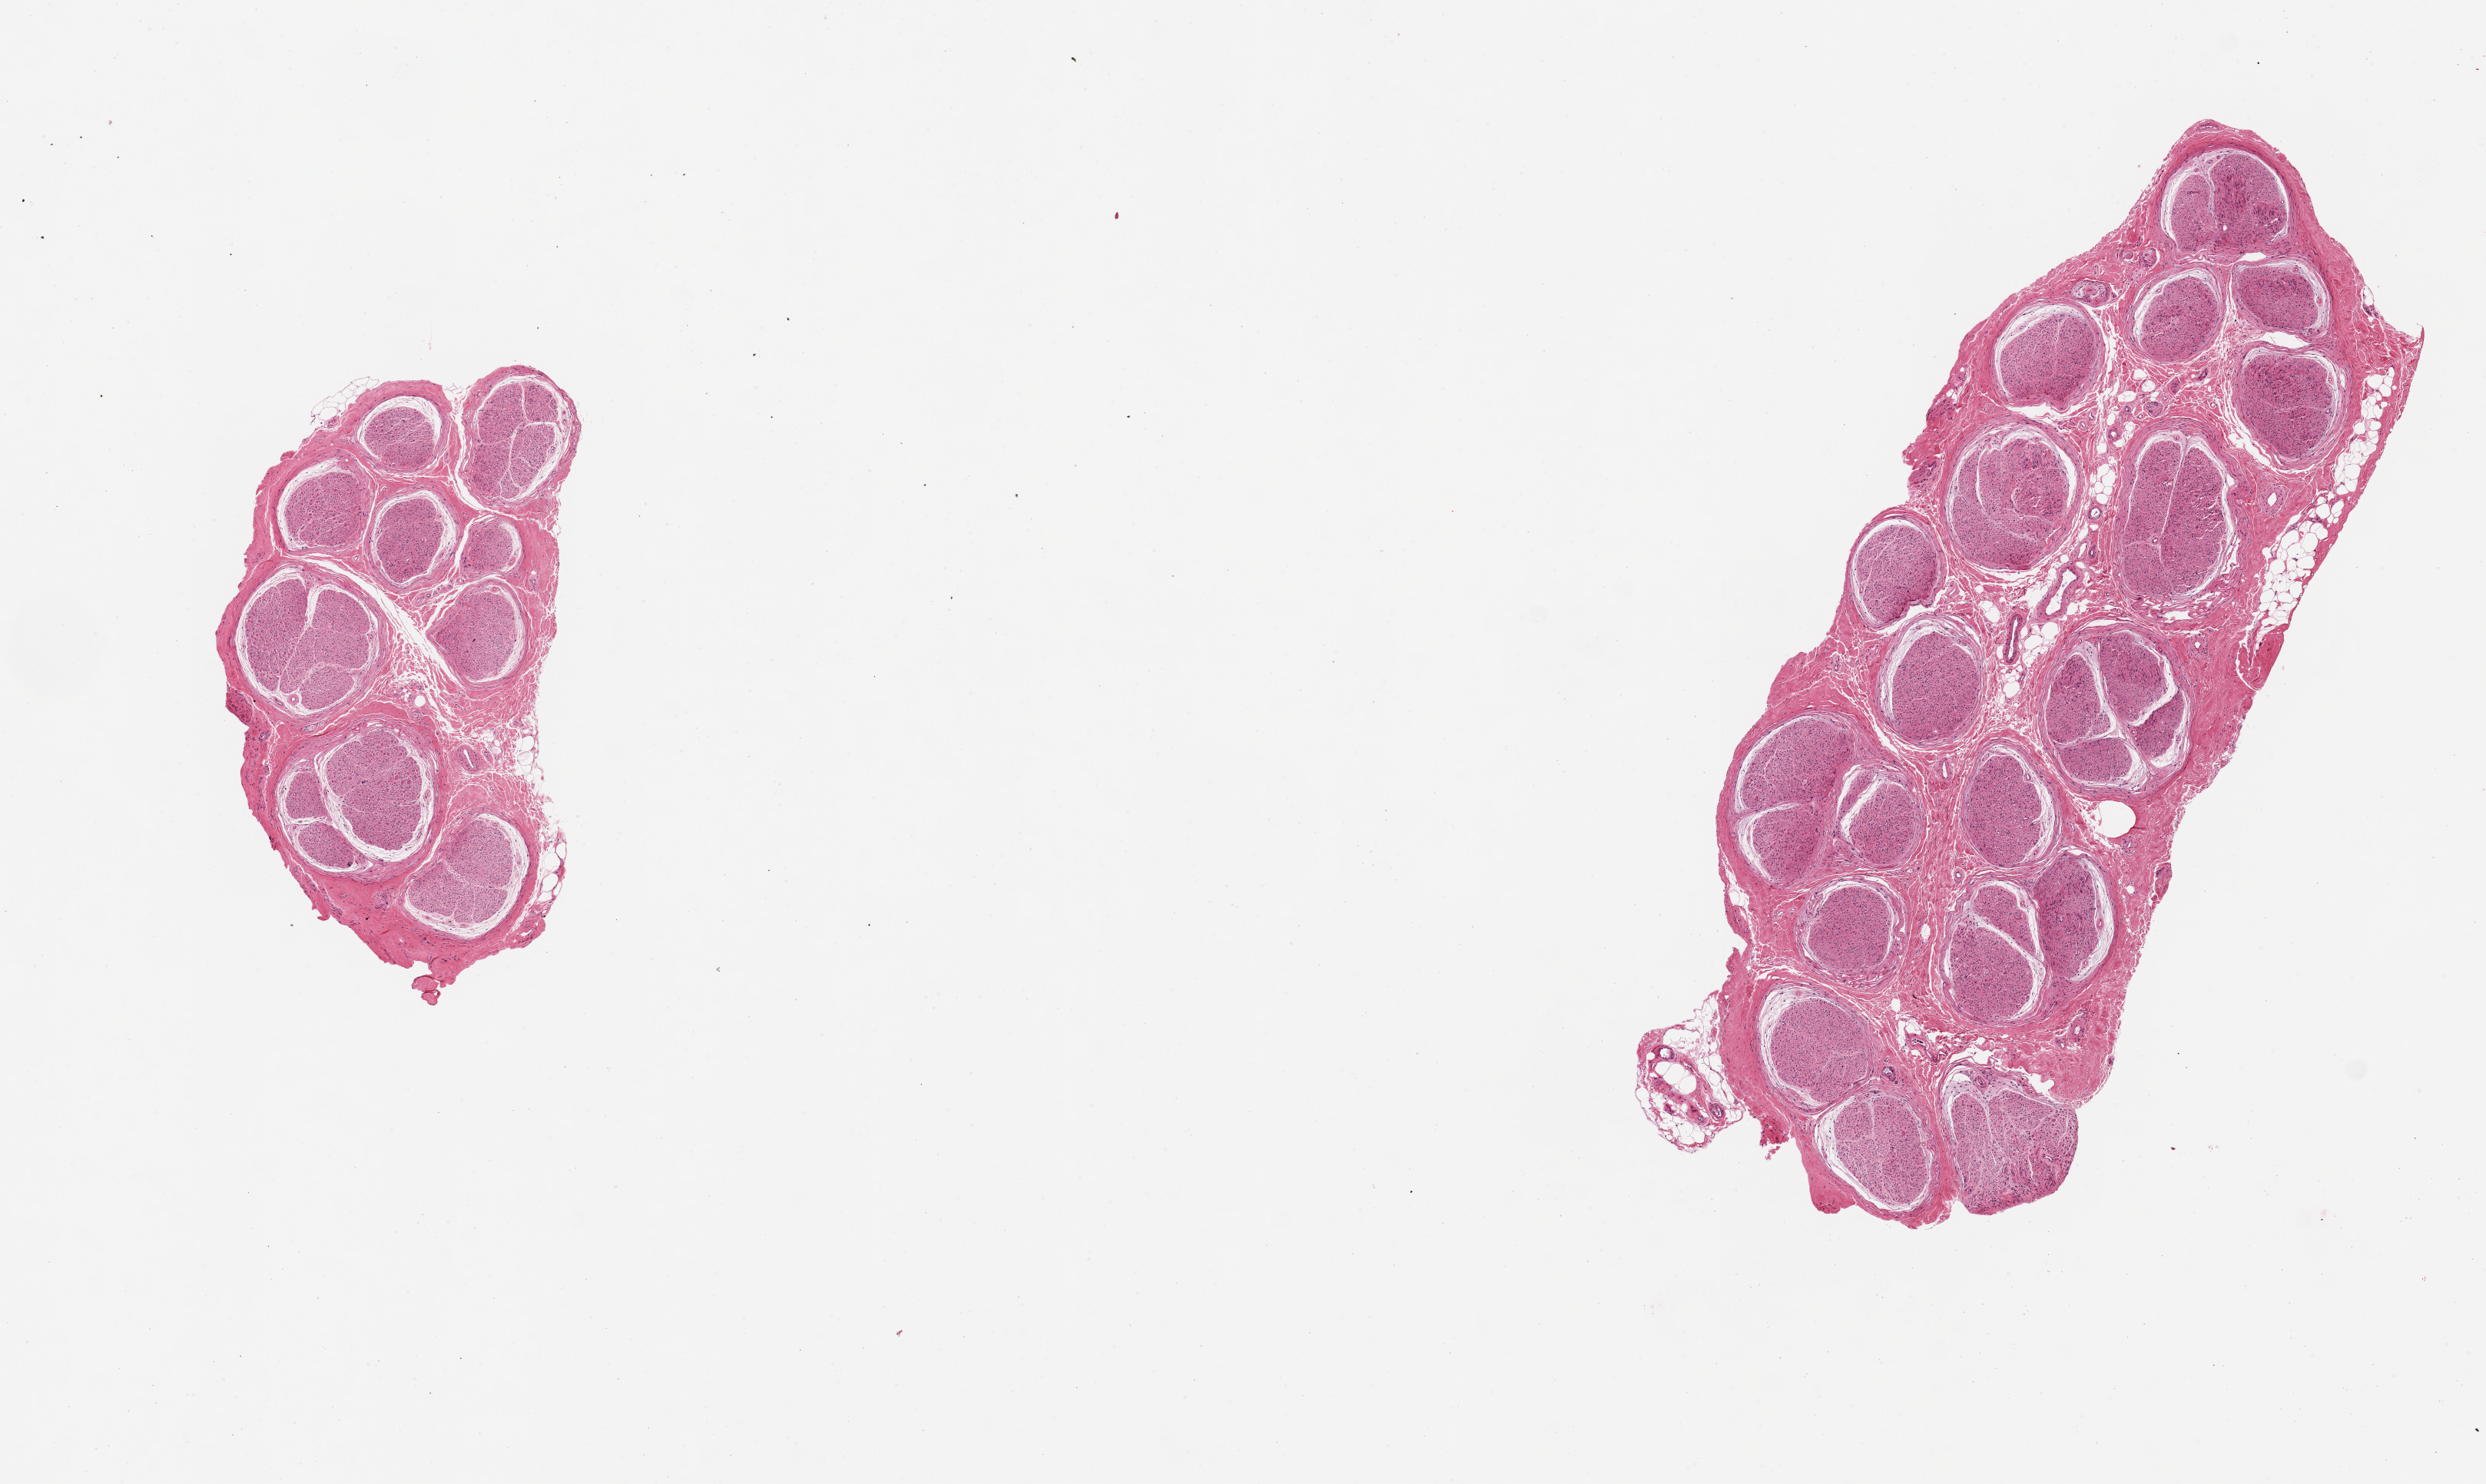
Whole-slide image, H&E stain, brightfield — shown as a low-resolution overview of the whole scanned area (about 12.8 x 7.6 mm, from a 20x scan); PAXgene-fixed paraffin-embedded (PFPE) section; section of tibial nerve (target tissue); donor tissue sample. Female donor.
Review note (as recorded): 2 pieces; well trimmed.